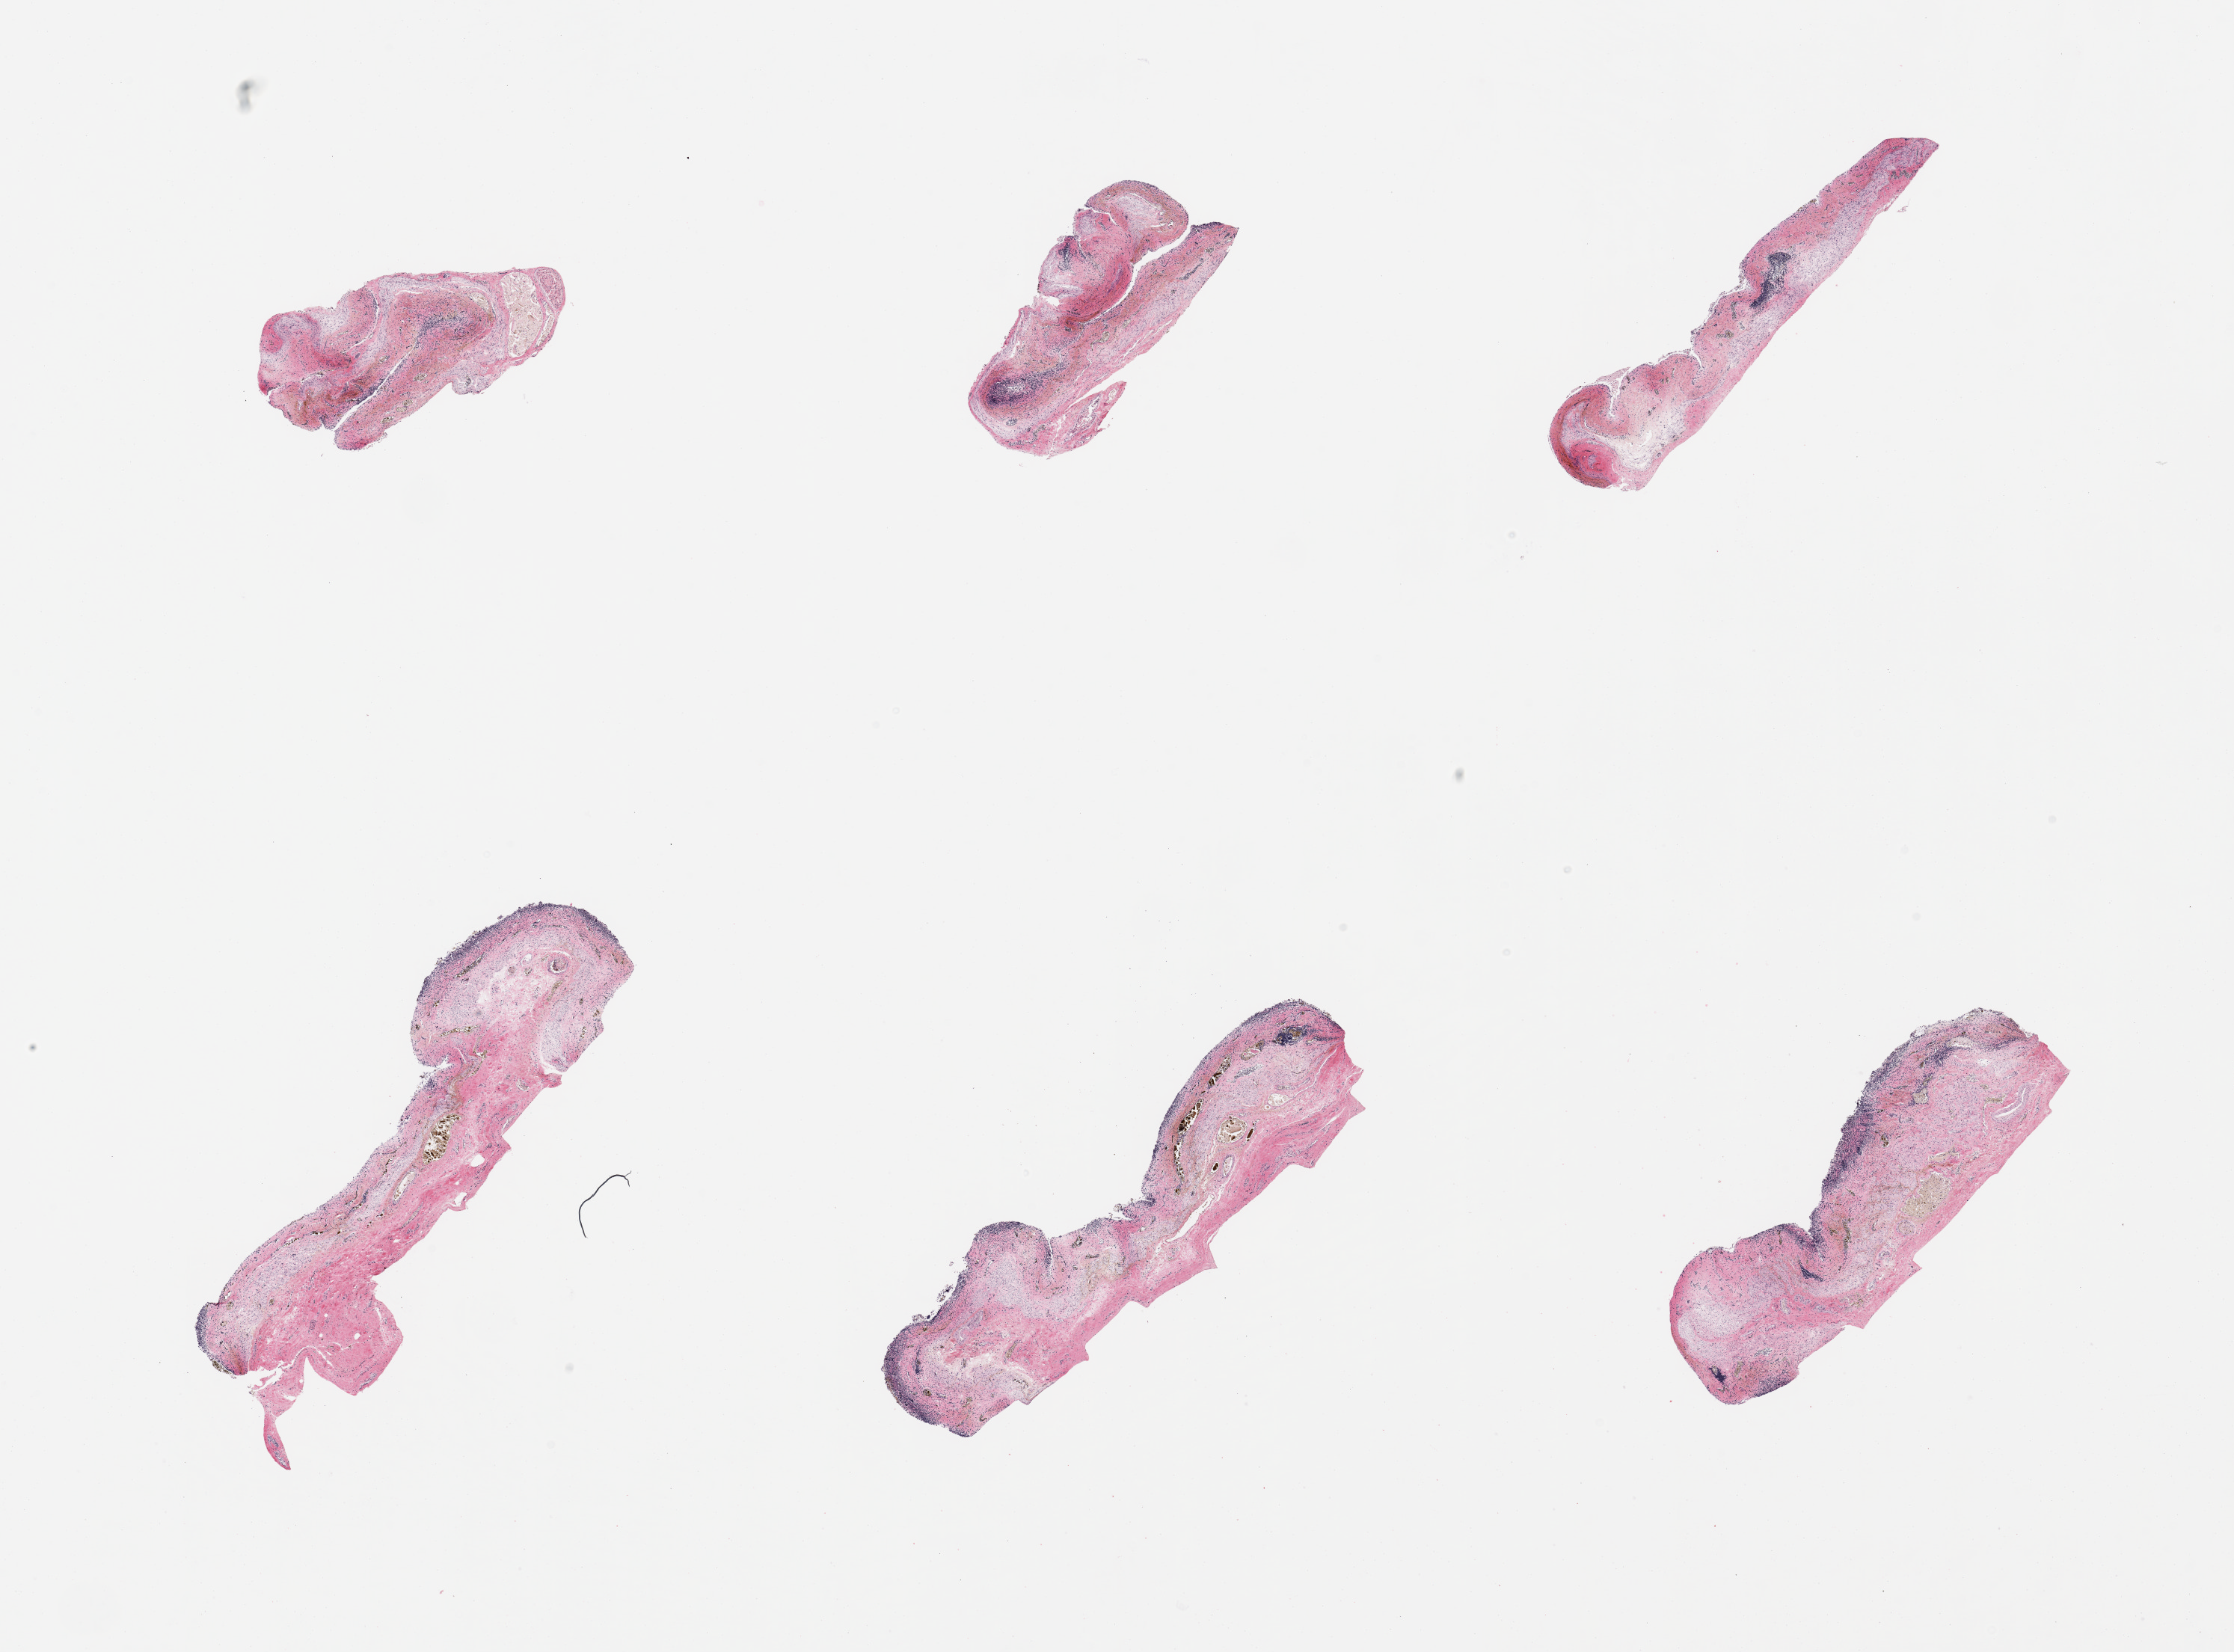
Digitized hematoxylin and eosin (H&E)-stained section, a low-resolution overview of the entire scanned area, about 23.6 x 17.5 mm (acquisition: 20x scan). PAXgene-fixed paraffin-embedded (PFPE) section. Target tissue: esophageal mucous membrane. Donor tissue sample. Male donor.
- reviewer comment on this tissue sample: 6 pieces, mucosa markedly autolyzed/sloughed